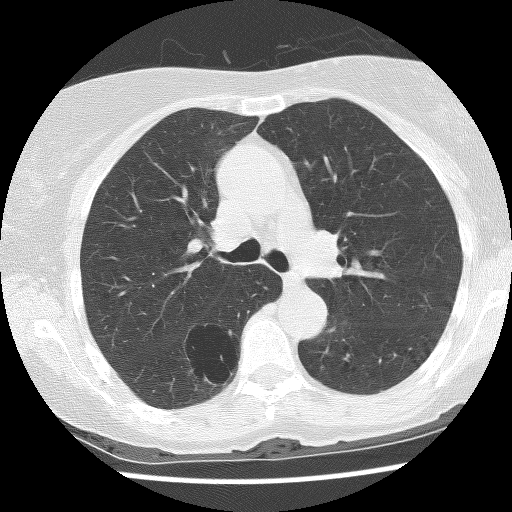
Chest CT (low-dose screening protocol), one axial image; baseline screening round; lung window (W 1500 / L -600 HU); 2.5 mm slice thickness; lung (sharp) reconstruction kernel (BONE); 120 kVp; slice 45 of 136 in the series; 512 × 512 image matrix. Female participant, aged 69 years at enrolment.
- Expert reader's lesion annotation, bounding box [x1, y1, x2, y2] px = [167, 322, 244, 396].
- The screening reader recorded 2 non-calcified nodules or masses ≥4 mm on this exam (right lower lobe, right lower lobe); which of them this box marks is not recorded.
- Lung cancer was diagnosed 288 days after this screen: non-small cell carcinoma, right lower lobe, poorly differentiated (G3), stage IB (AJCC 6th edition), 36 mm at pathology.